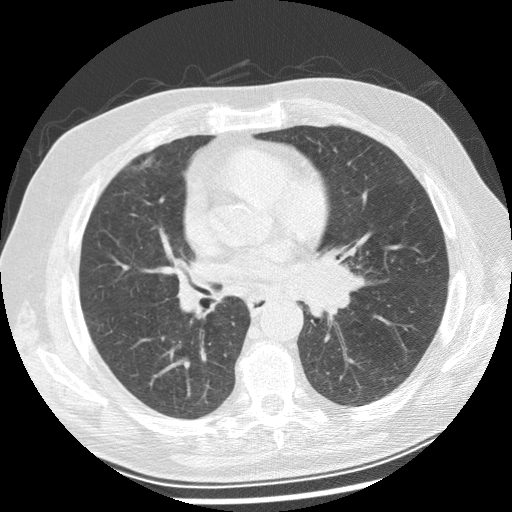
Low-dose screening chest CT, one axial slice. Position 131 of 250 along the scan axis. Lung window (W 1500 / L -600 HU). 512 × 512 image matrix, field of view 360 × 360 mm.
Structures marked on this image (outlined manually by an expert reader):
- lesion 1 (tumor, left main bronchus): bounding box <301,257,368,319> (left, top, right, bottom; pixels)